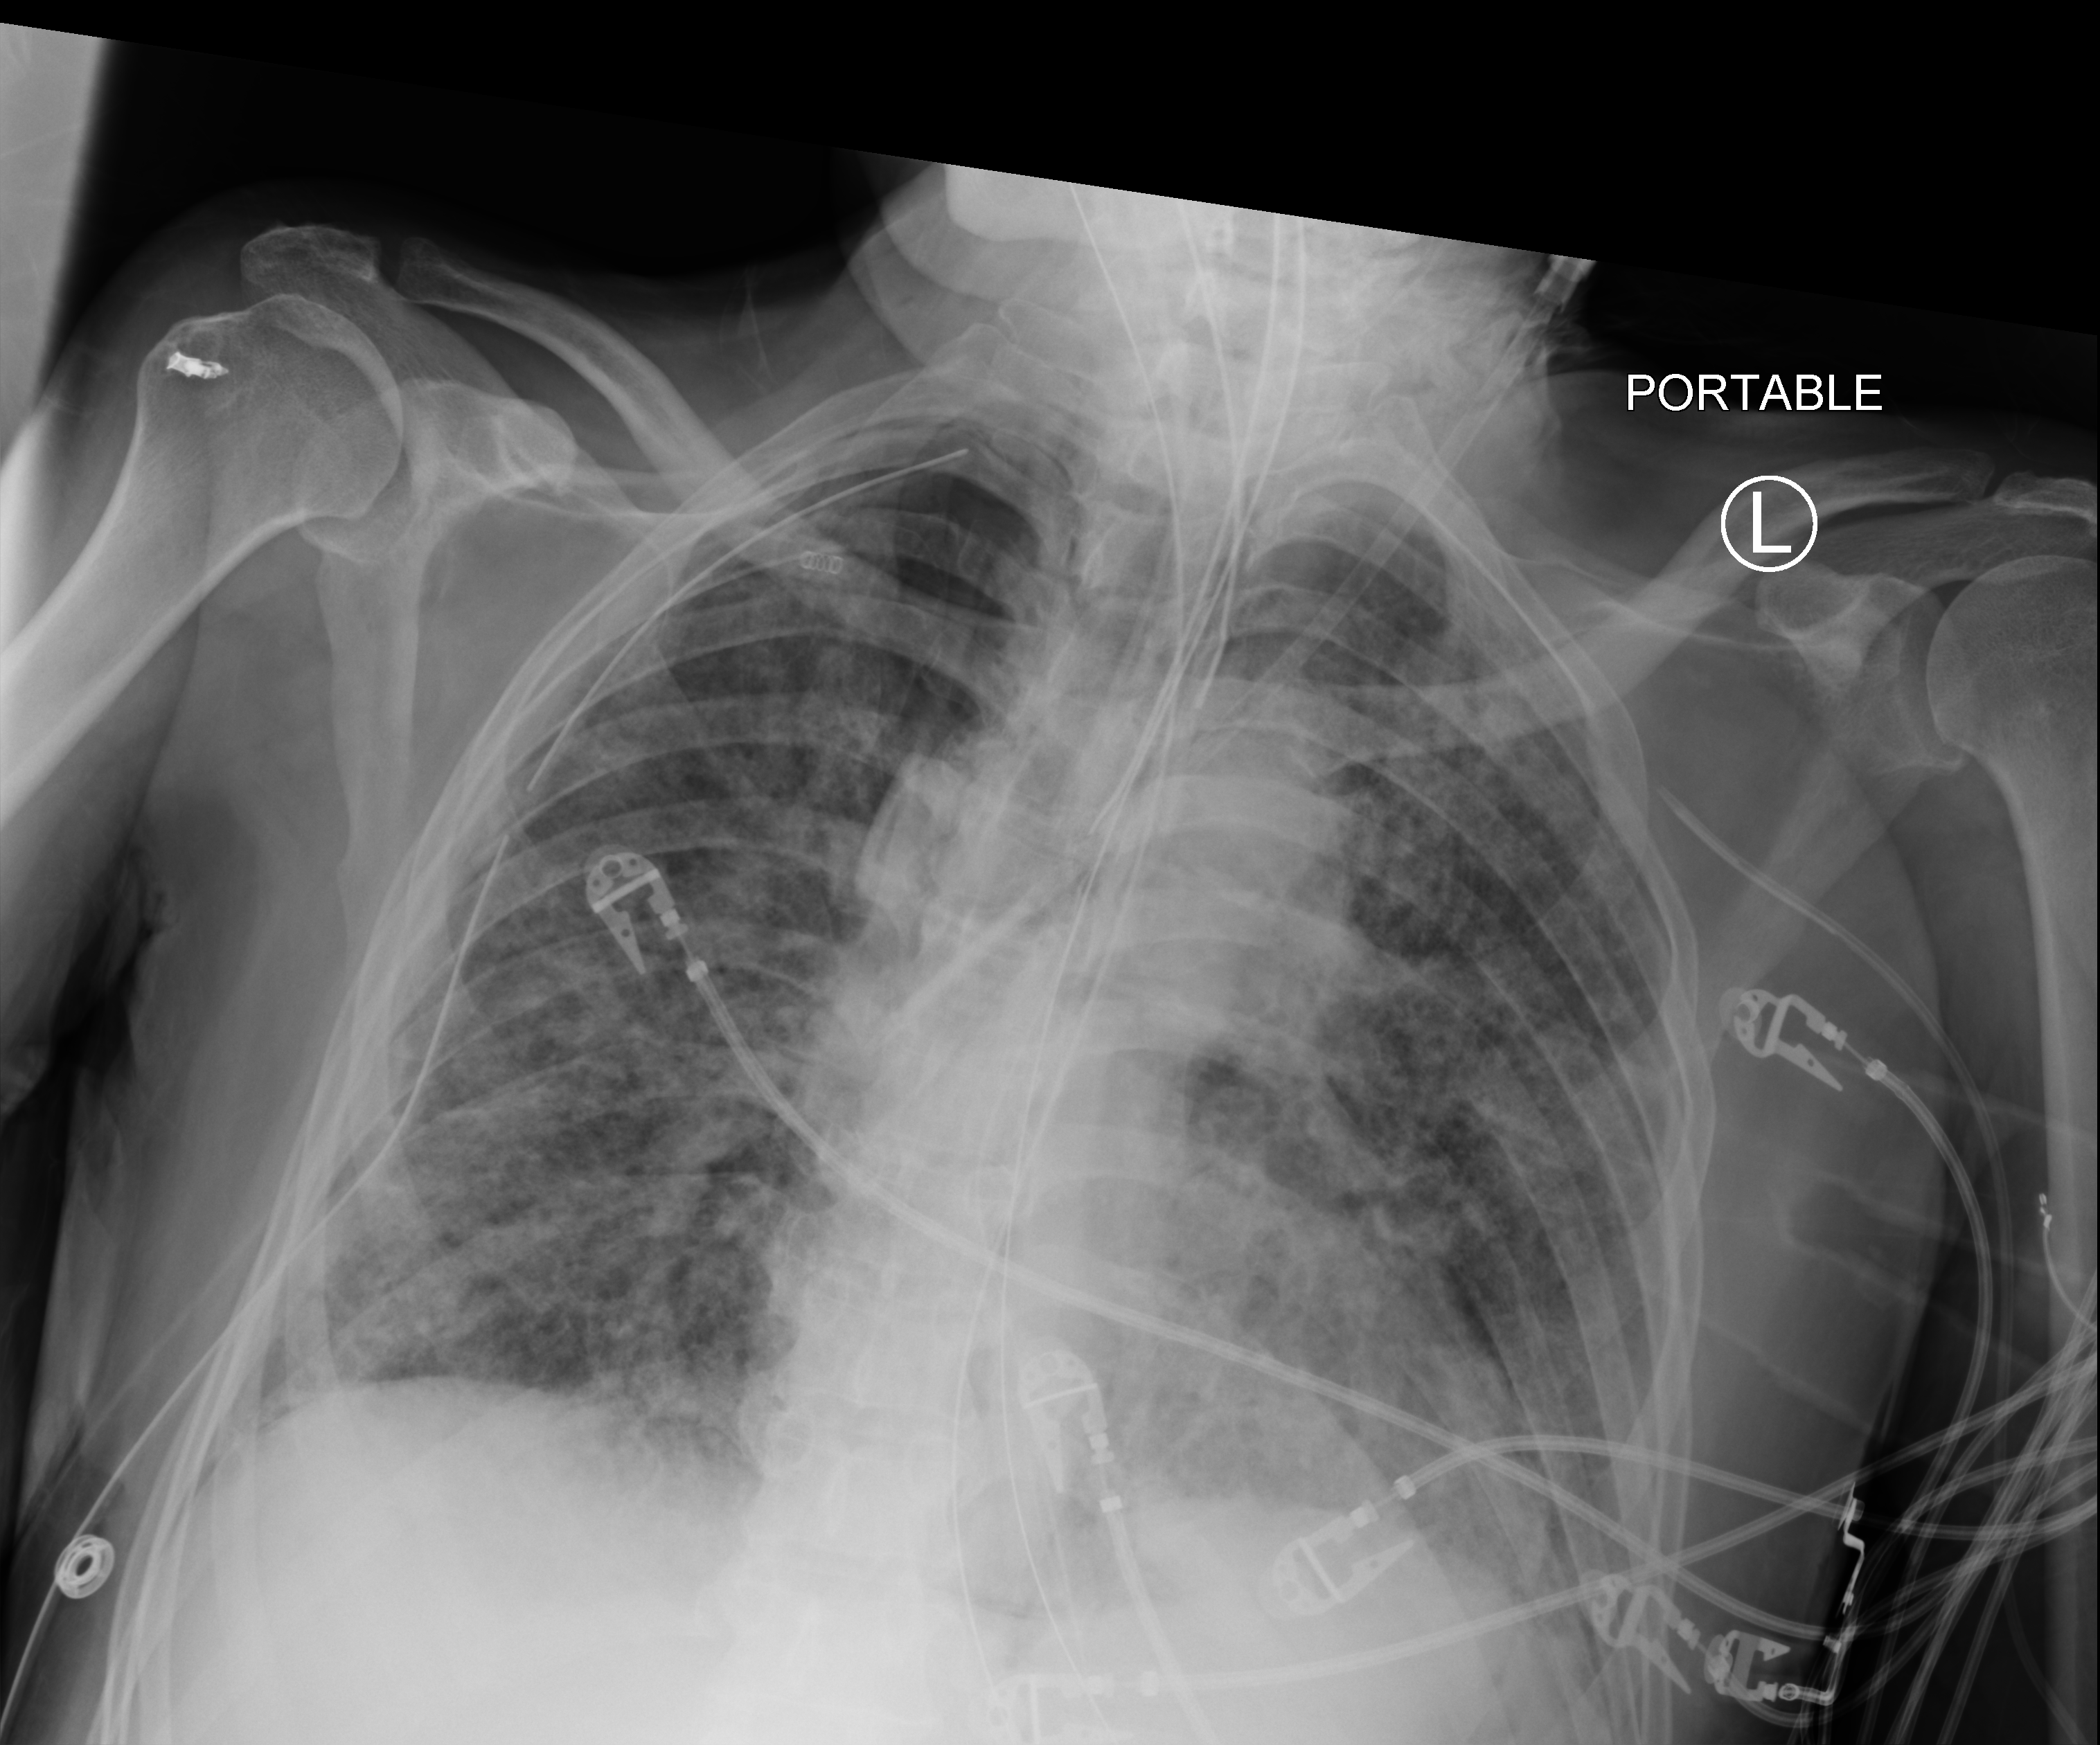
Bedside chest radiograph (computed radiography). Patient hospitalised with COVID-19; male, aged 60–74 years.
Hospital-stay facts (about this admission, not read from this image; timing relative to this image not recorded):
- admitted to intensive care during this hospital stay: yes